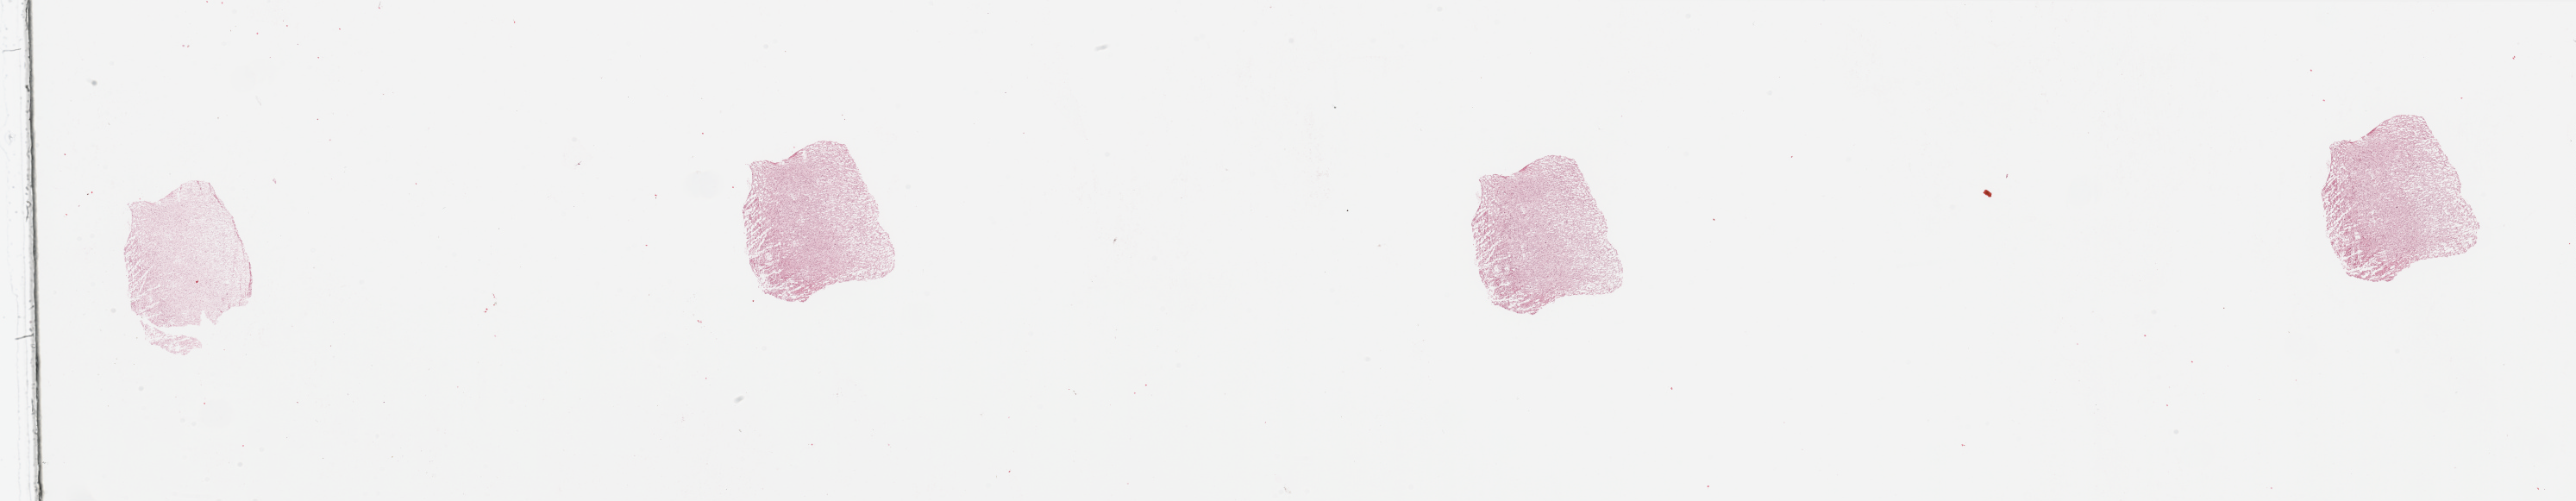
Whole-slide histology image, Hematoxylin and eosin (H&E) stained, shown as a low-resolution overview of the whole scanned area (about 47.3 x 9.2 mm). Tumour tissue sample, sampled site: occipital cortex. Patient: male, age 73 years. Composition of this section per pathologist review: tumour nuclei 80%, necrosis 0%.
Primary tumour site (as recorded): occipital lobe. Diagnosis: Glioblastoma.